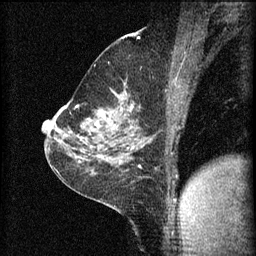
Breast MRI (dynamic contrast-enhanced), one sagittal slice. Slice 38 of 60 in the series (ordered by position). 3 images stored at this slice position (order not interpretable as contrast timing). 1.5 T. TE 4.2 ms, TR 8.2 ms. 2 mm slice thickness. 256 × 256 image matrix, field of view 180 × 180 mm. Female patient, age 59 years.
Outlined on this slice (semi-automatically segmented with operator editing):
- analysis volume of interest (the breast-tissue region the enhancement analysis was run in; not a lesion): bounding box <78,92,137,135> (left, top, right, bottom; pixels)
- tumour enhancement mask (voxels above the 70 % enhancement threshold inside the analysis volume of interest): <88,112,103,127>